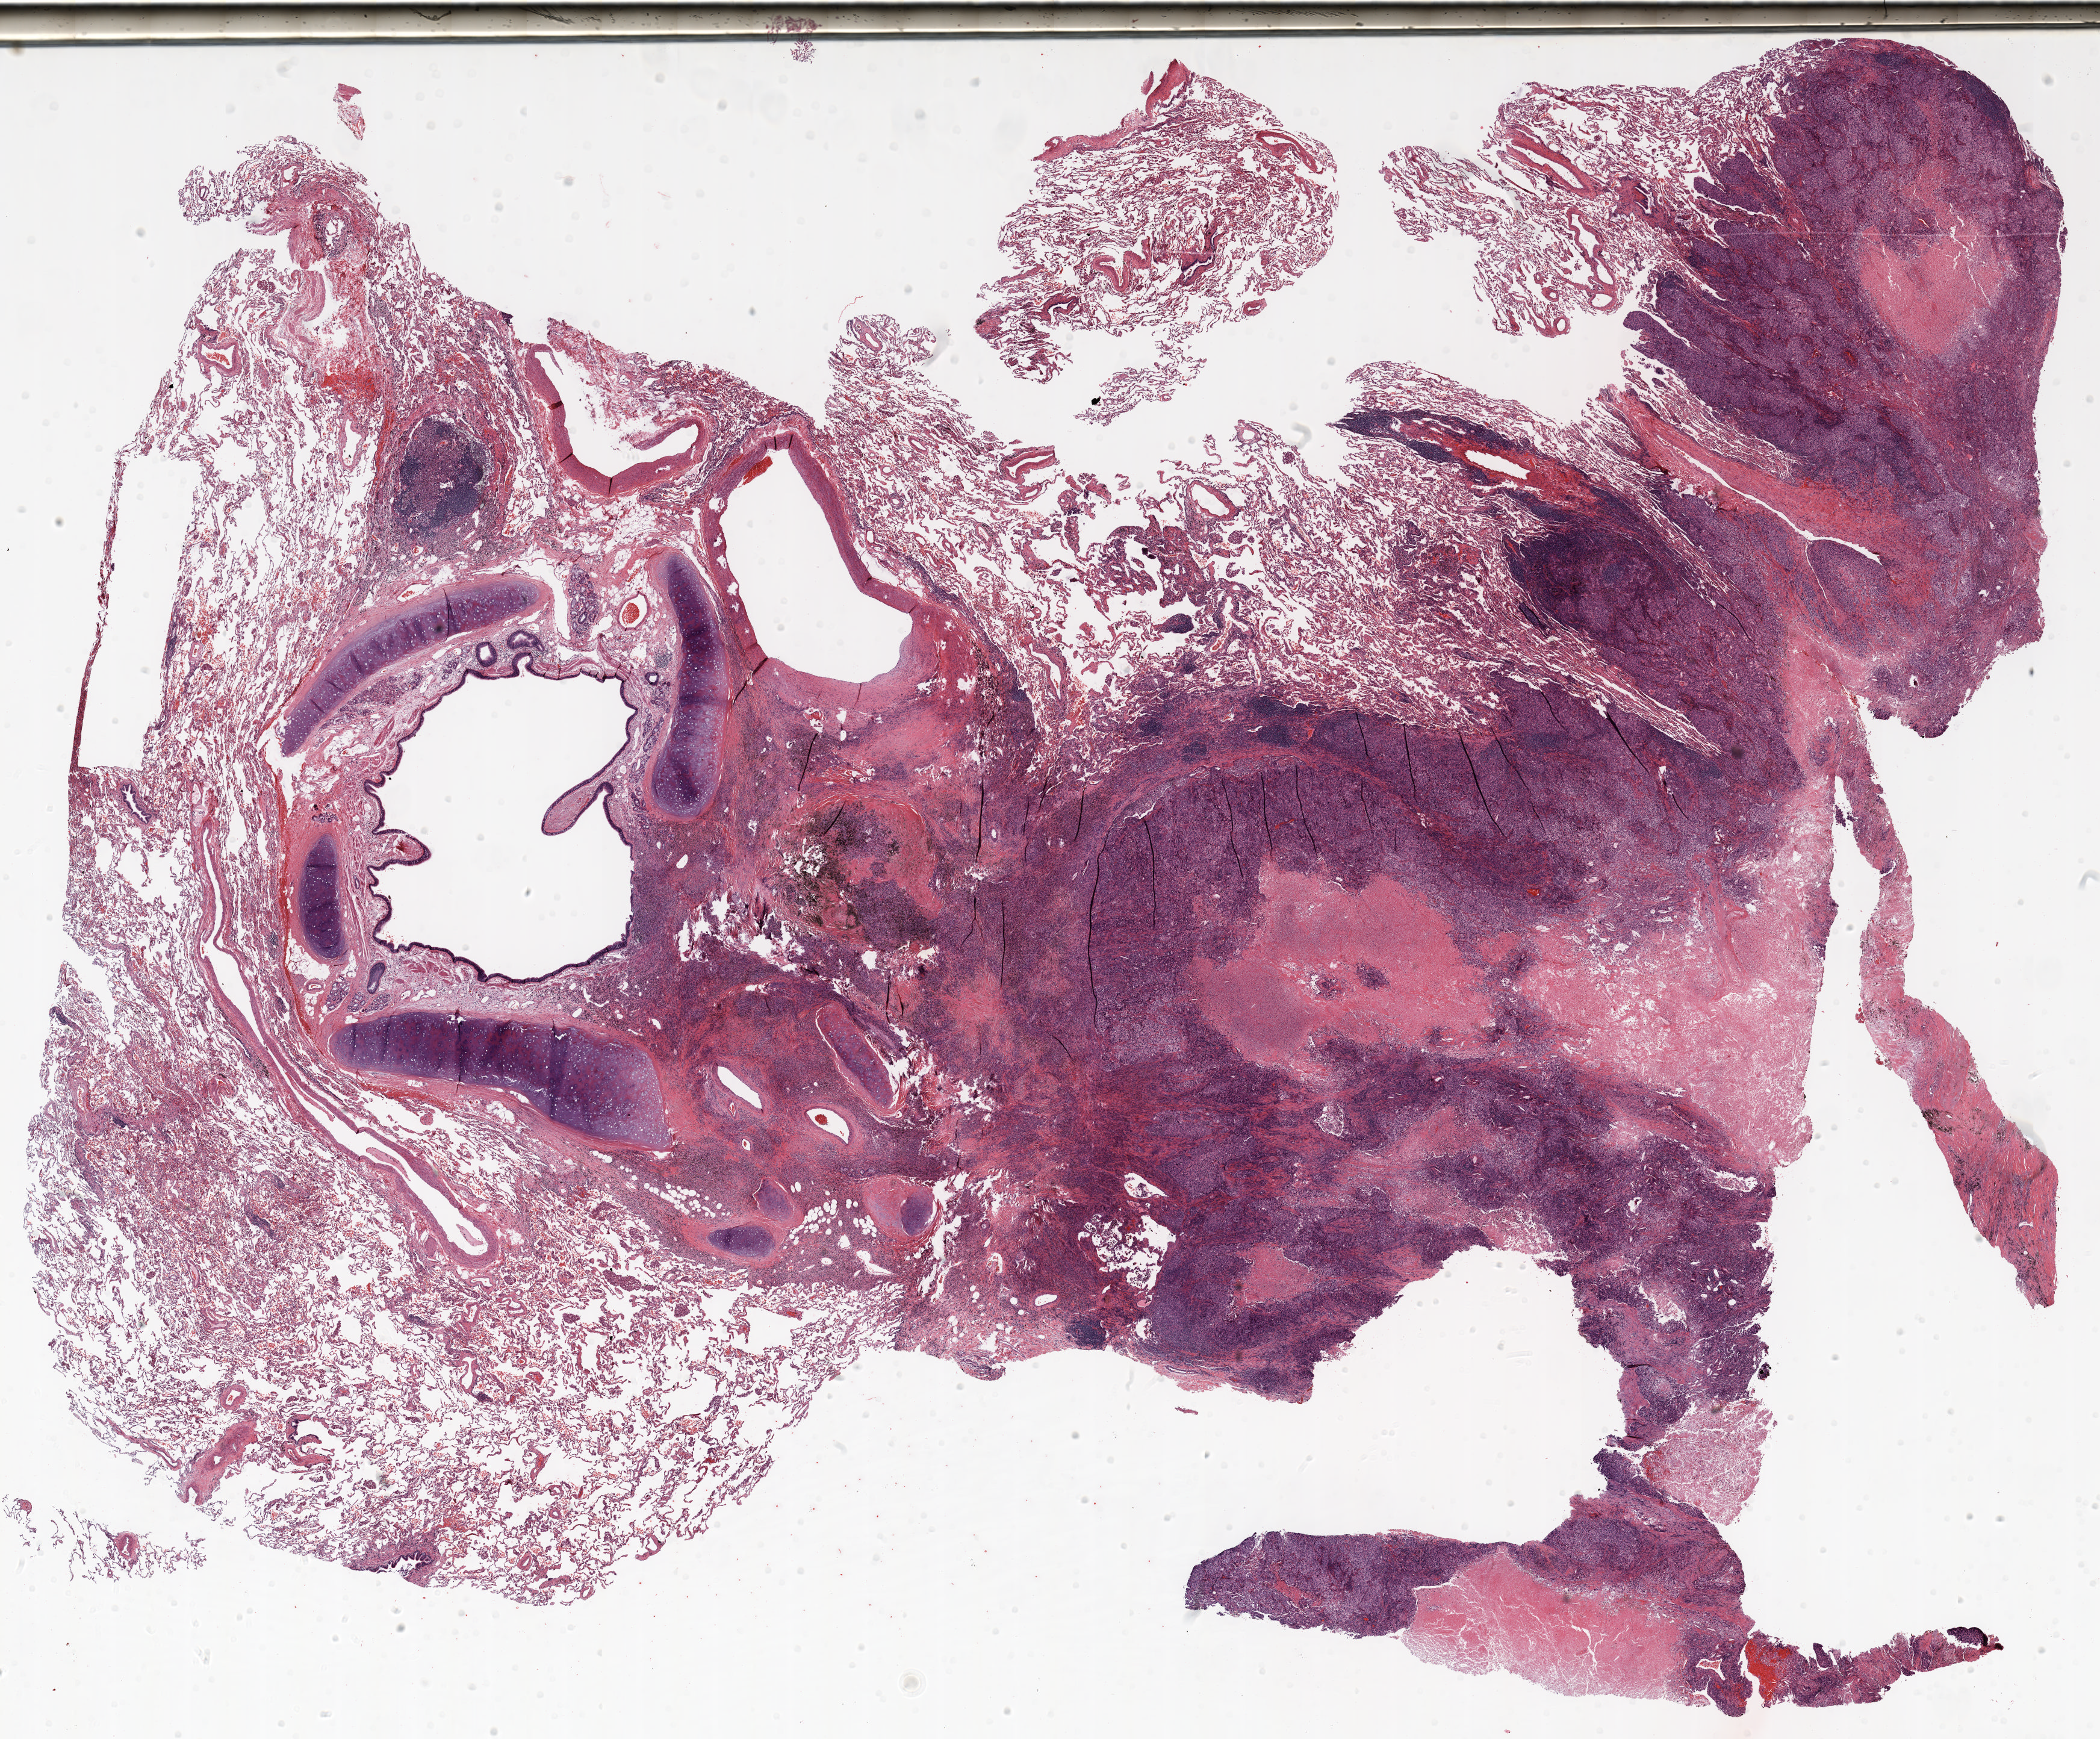
Whole-slide histology image, H&E-stained, a low-resolution overview of the entire scanned area, about 28.0 x 23.2 mm. Formalin-fixed paraffin-embedded (FFPE) section. Lung. Male patient, aged 69 at enrolment. Current smoker at enrolment. Grade: poorly differentiated (G3).
Tumour size (pathology): 40 mm. Primary tumour location (clinical record): right upper lobe. ICD-O-3 topography: upper lobe of lung (C34.1). Stage (AJCC 6th edition): IB. Participant's lung-cancer diagnosis: Adenocarcinoma, NOS (ICD-O-3 8140/3).